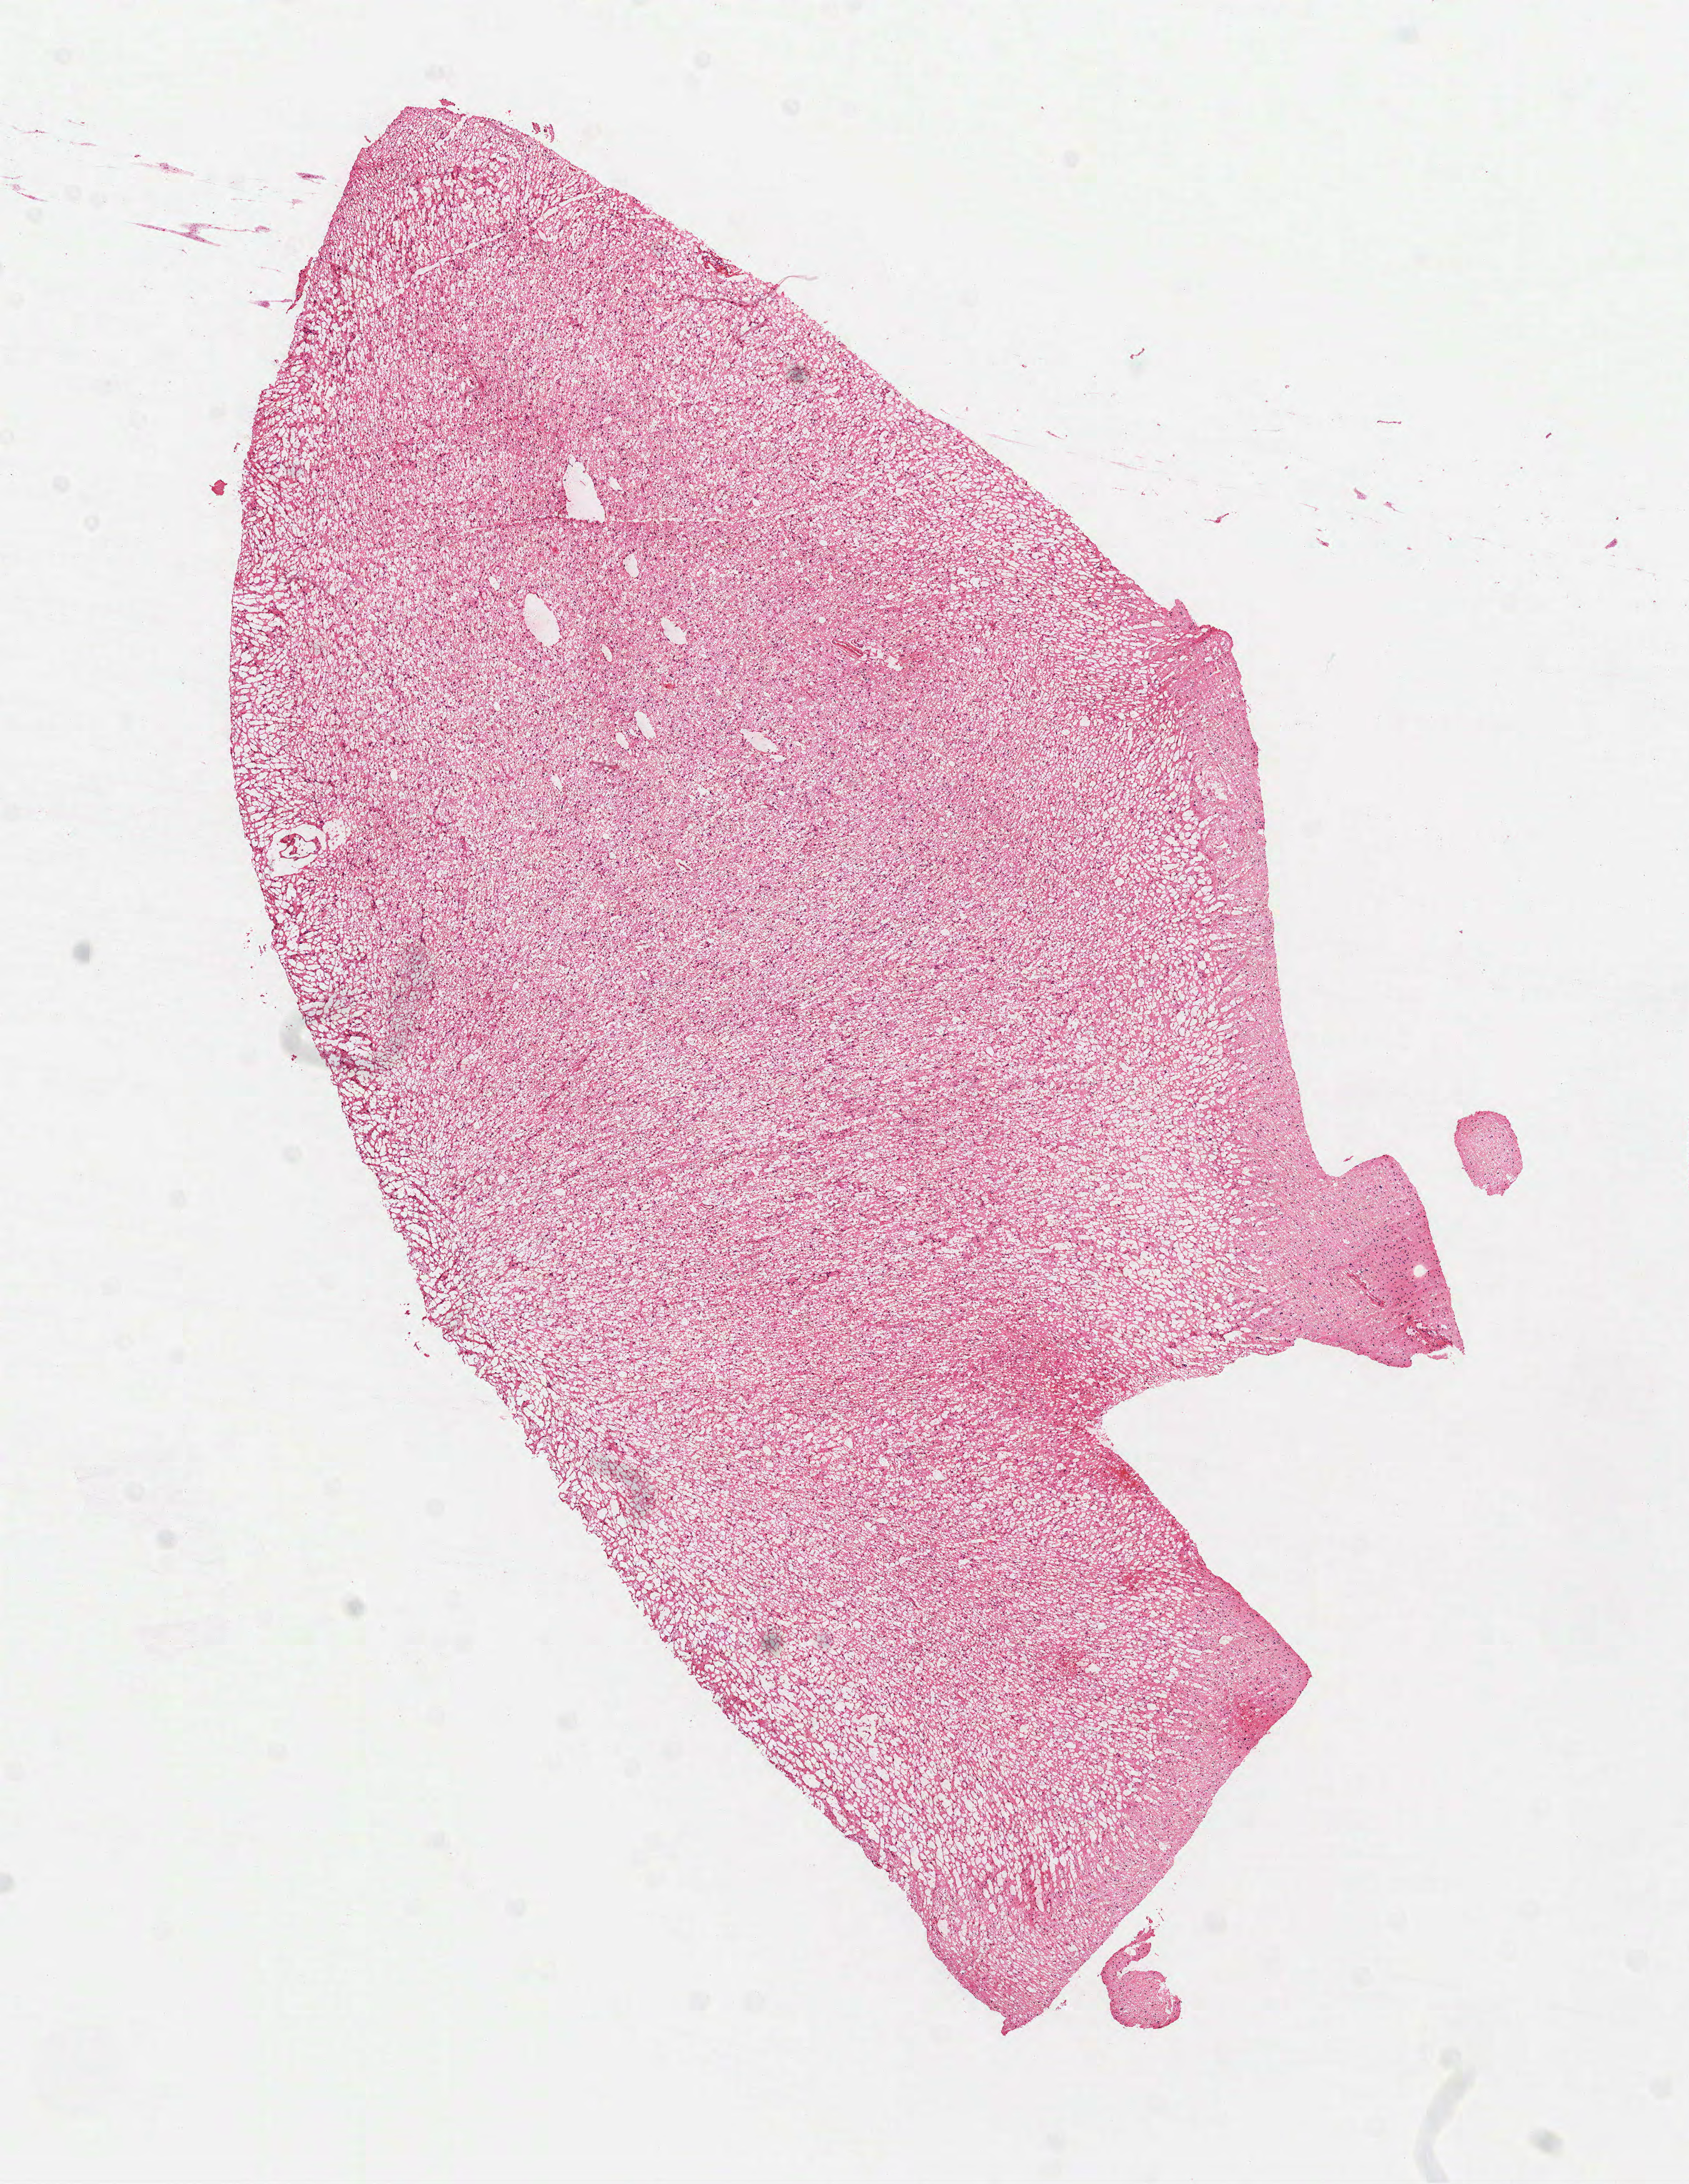
Digitized Hematoxylin and eosin (H&E) stained tissue section (whole slide) — shown as a low-resolution overview of the whole scanned area (about 9.5 x 12.3 mm, from a 40x scan); frozen section from the top of the tissue portion; sample: primary tumour, brain. Male patient; age at initial diagnosis 41 years. Histologic grade: G2 (moderately differentiated). Pathologist review of this section (percent, as recorded): tumour cells 100%, tumour nuclei 75%, normal cells 0%, stromal cells 0%, necrosis 0%.
Laterality: left. Diagnosis: Mixed glioma (cerebrum).